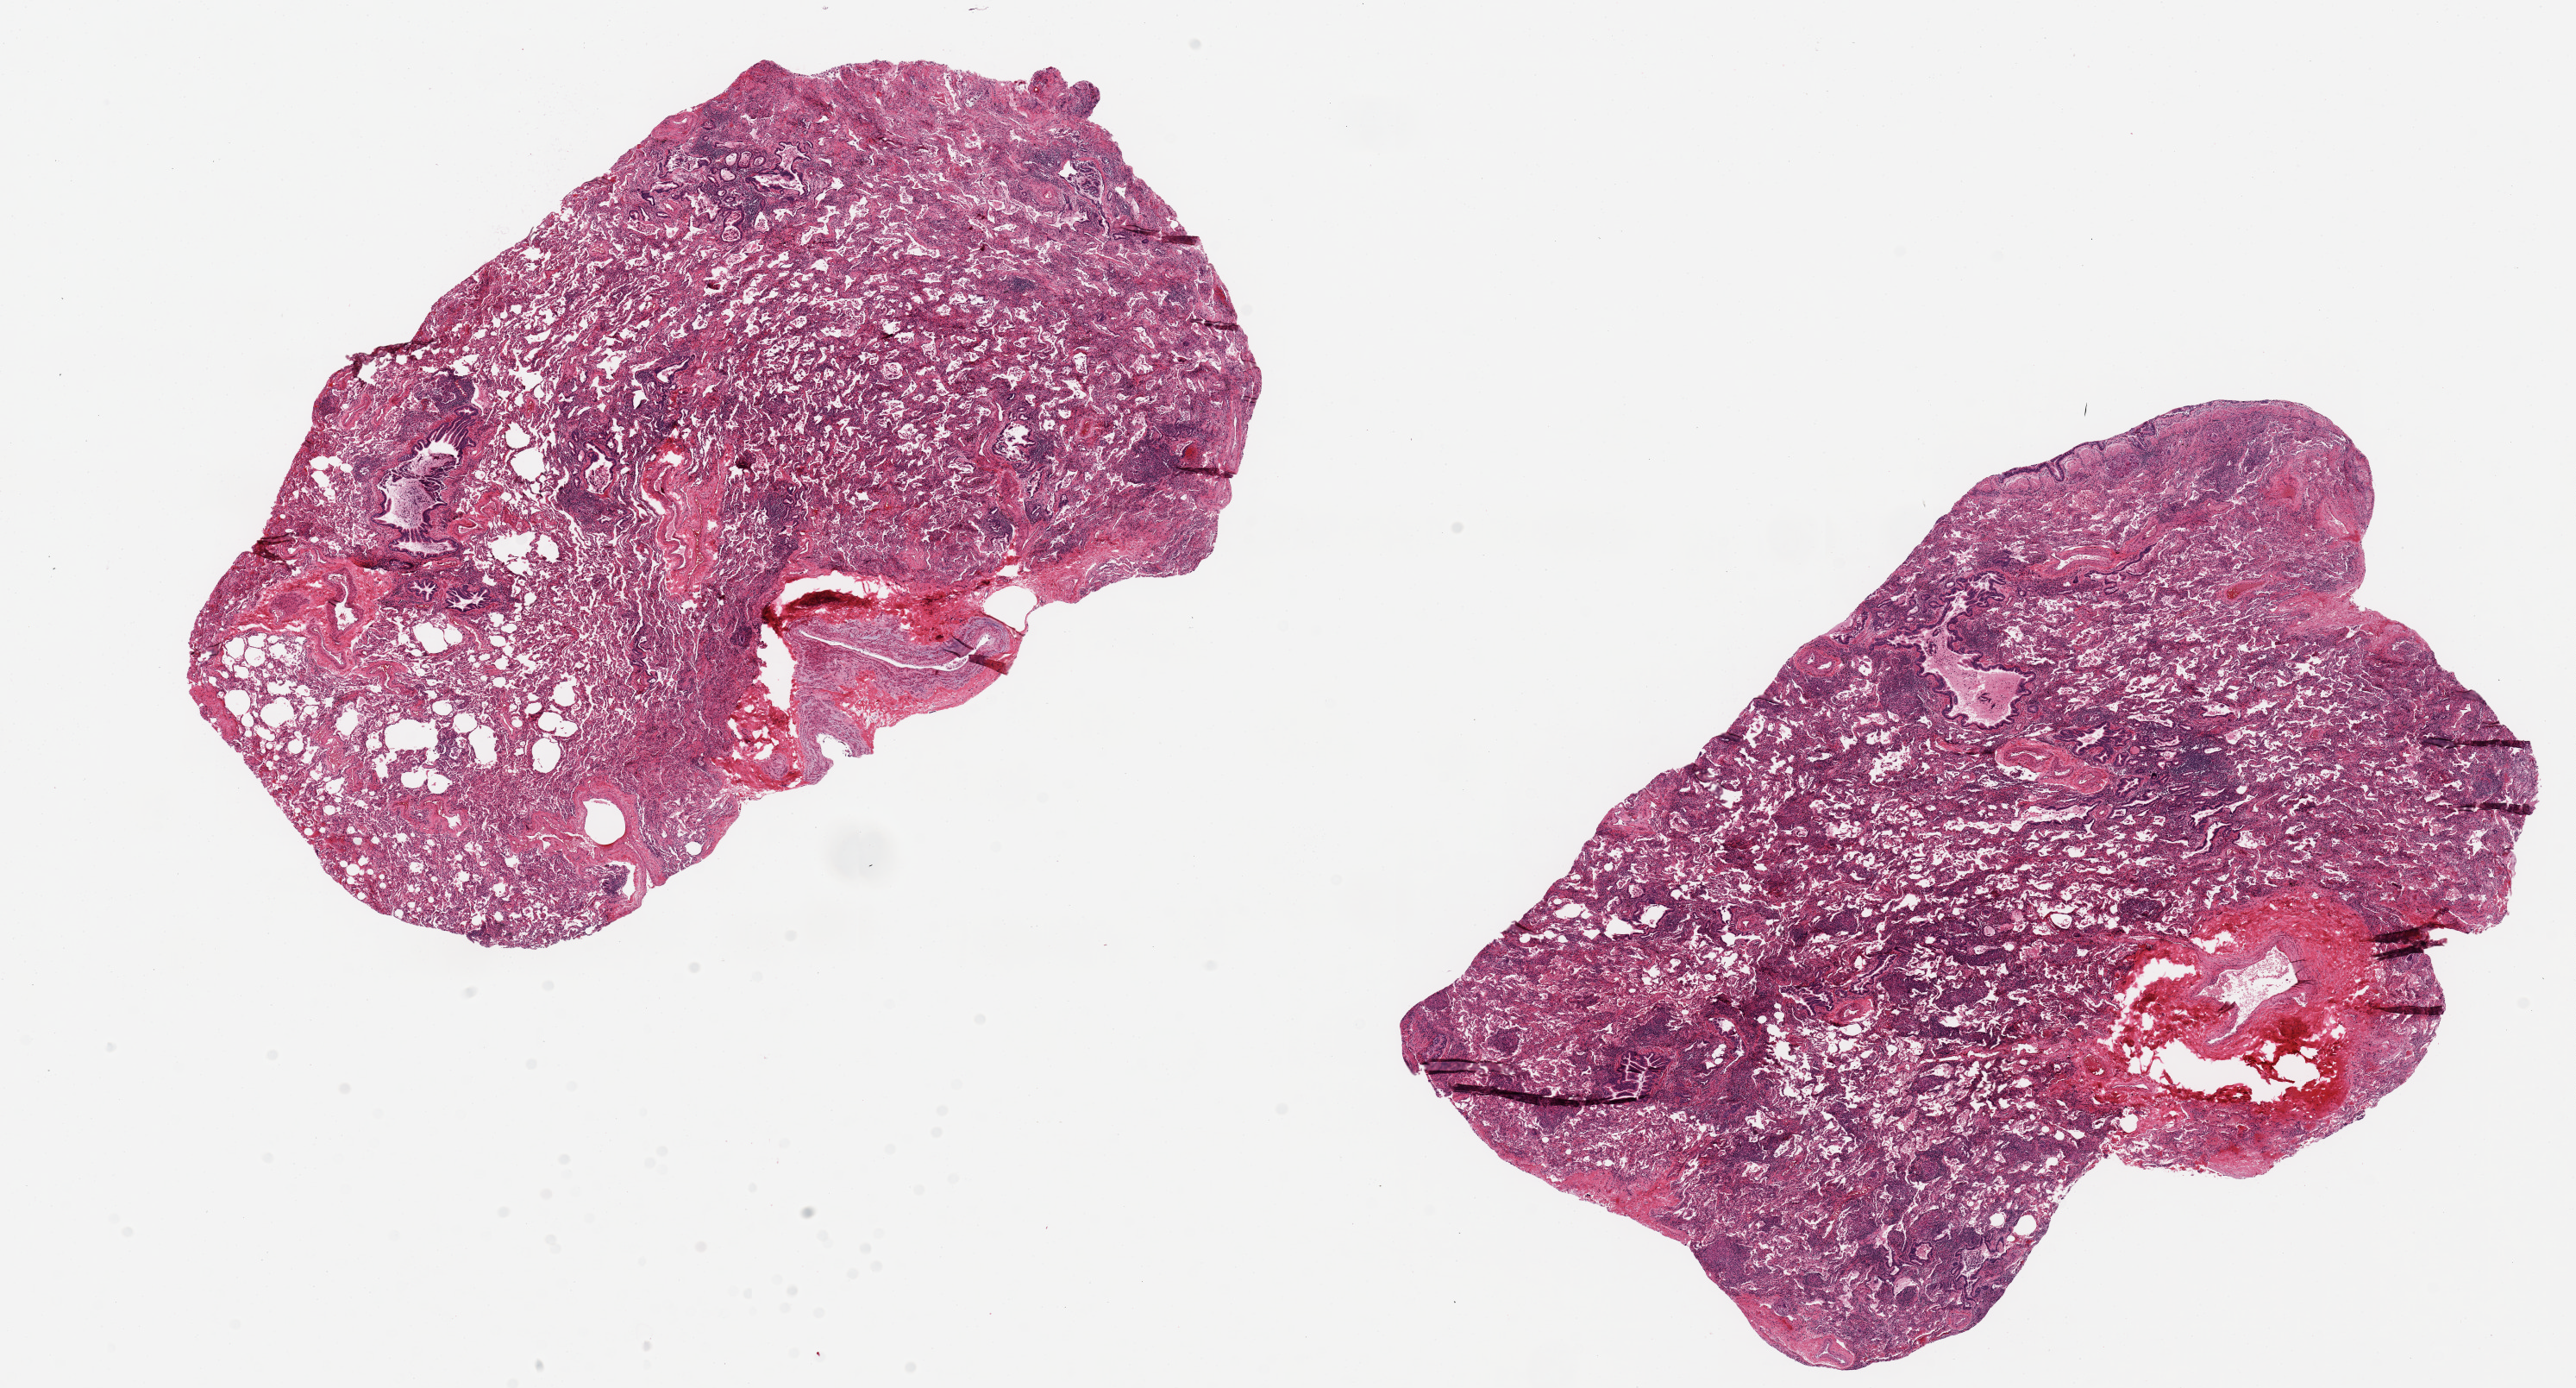
H&E whole-slide image, brightfield — low-resolution overview of the scanned area, about 23.6 x 12.7 mm (from a 20x scan); PAXgene-fixed paraffin-embedded (PFPE) section; sampled site (target tissue): lung; tissue donor sample. Male donor.
* reviewer comment on this tissue sample: 2 pieces, 9.5x6 & 10x7mm; giant cell granulomas and interstitial fibrosis c/w sarcoidosis (clinical history of sarcoid)